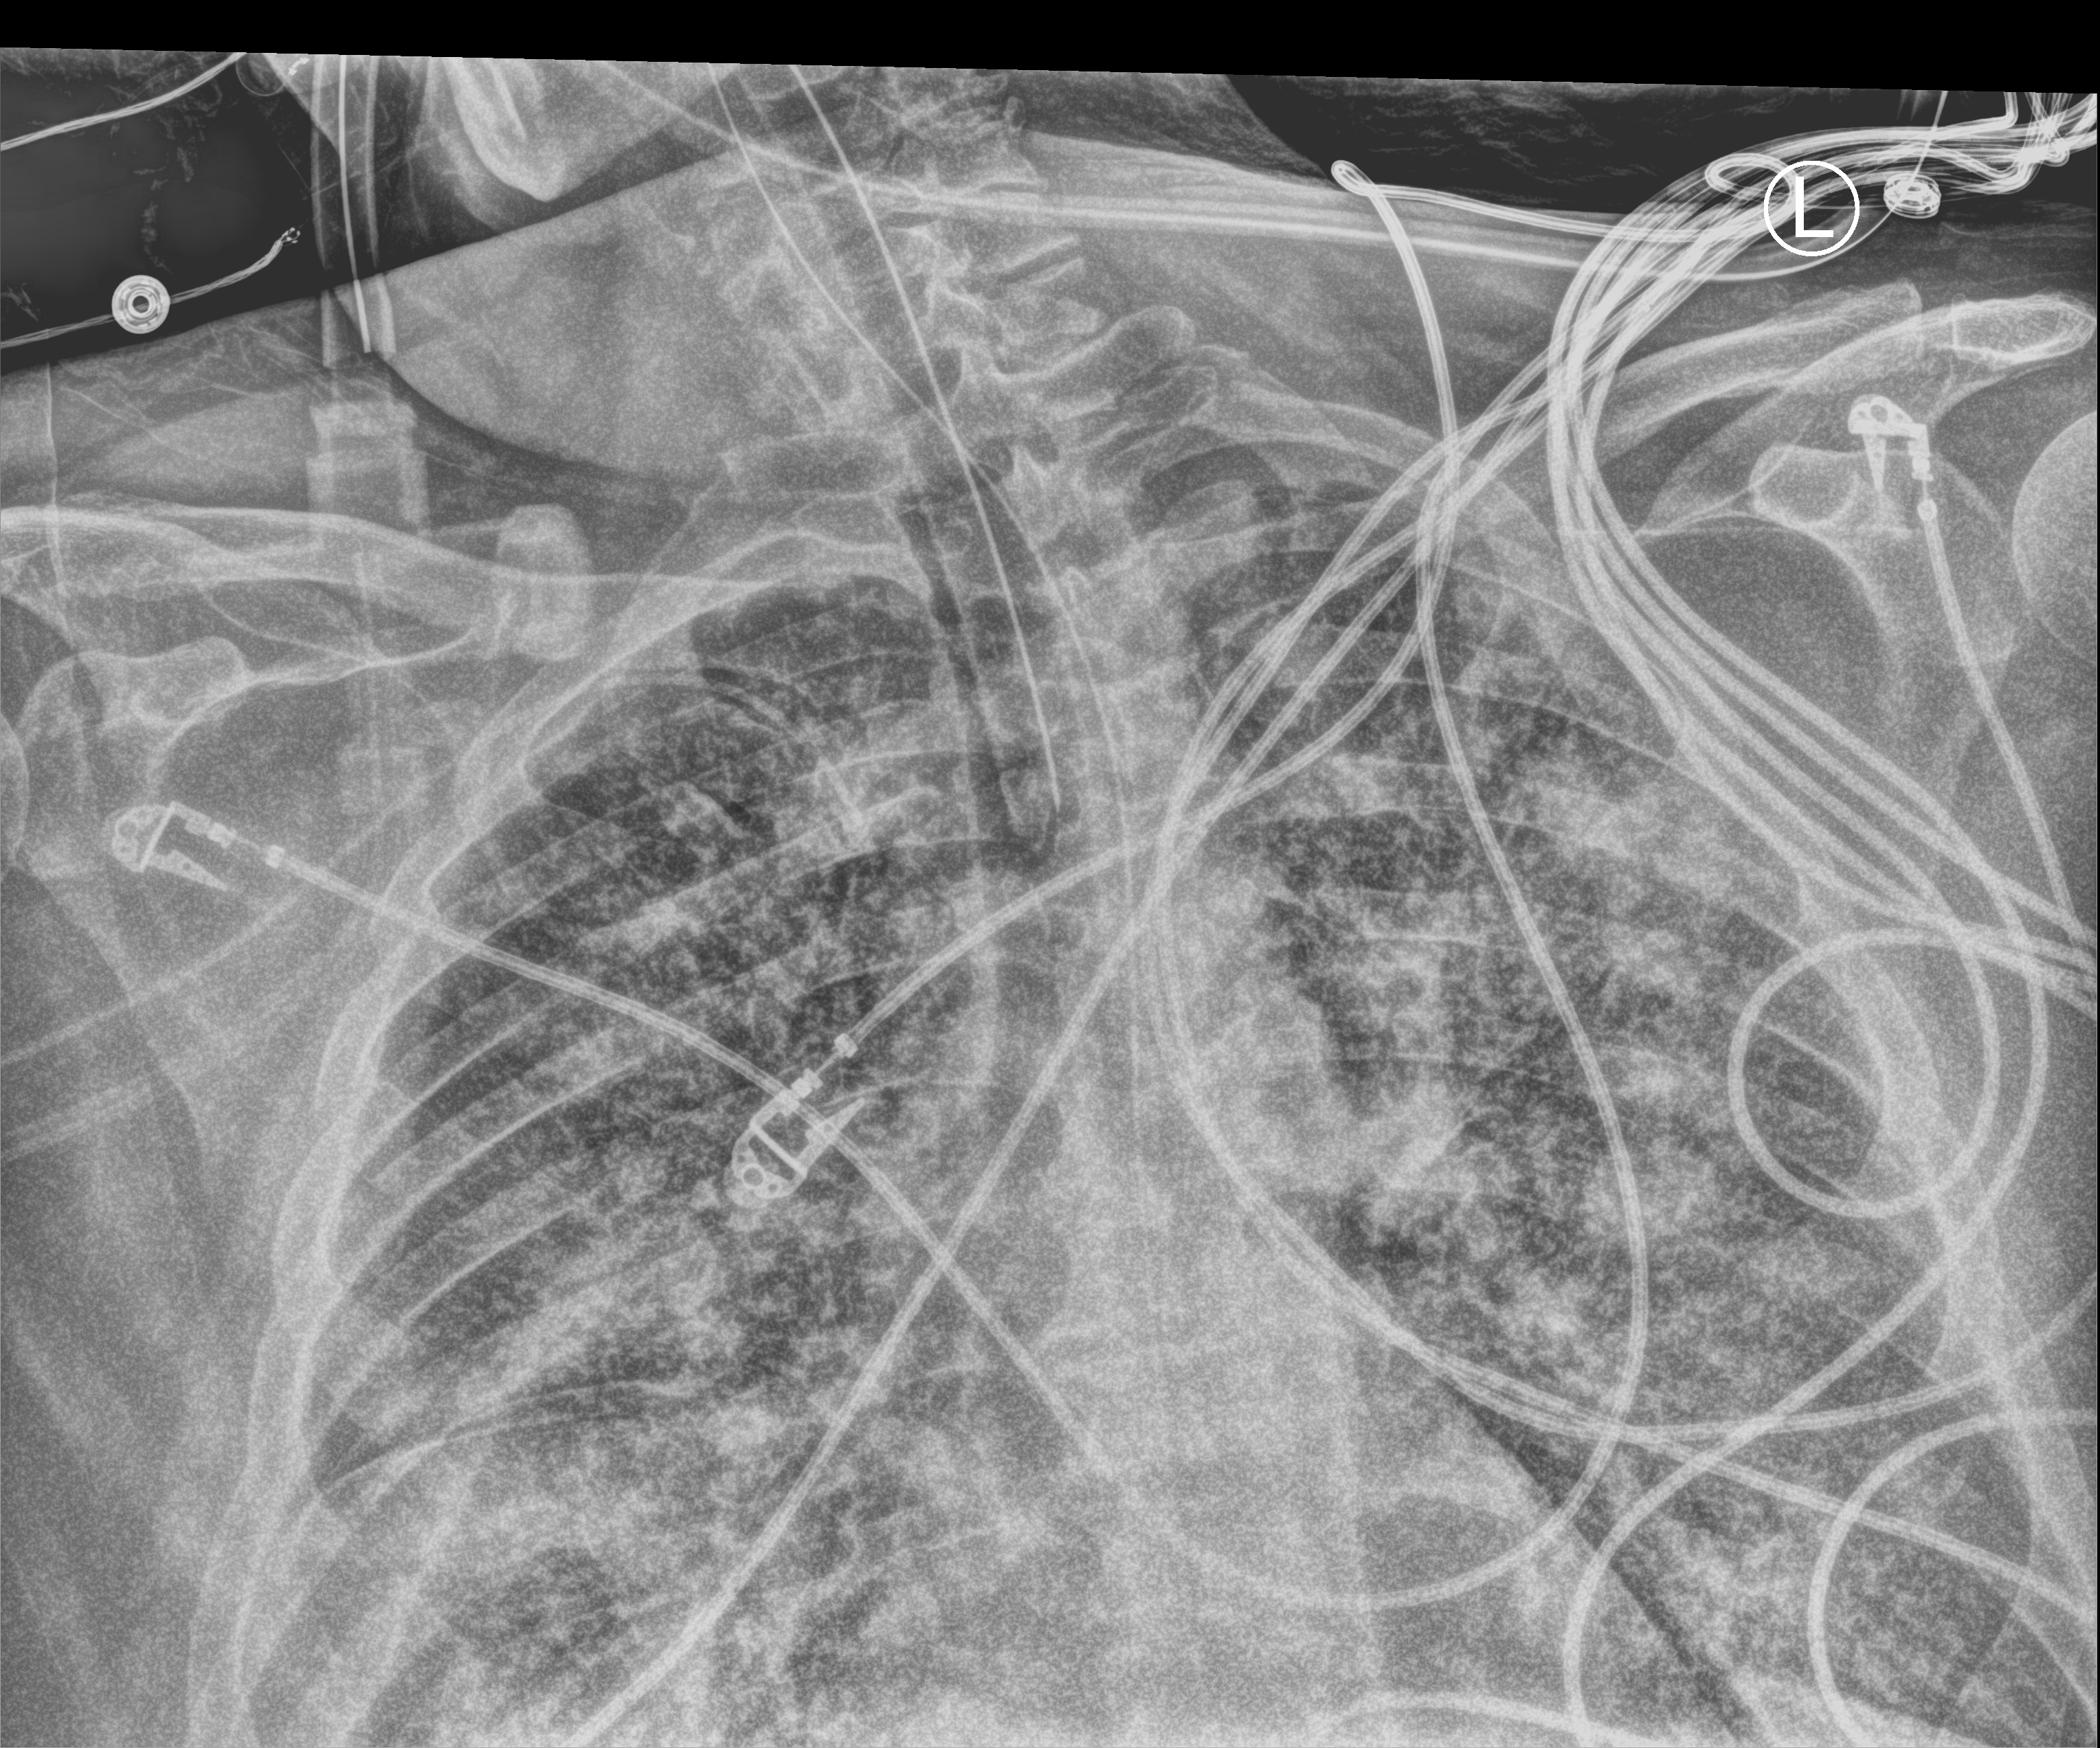
Bedside chest radiograph (computed radiography). Male patient hospitalised with COVID-19, age 60–74 years.
Hospital-stay facts (about this admission, not read from this image; timing relative to this image not recorded): smoking status (admission record): former.